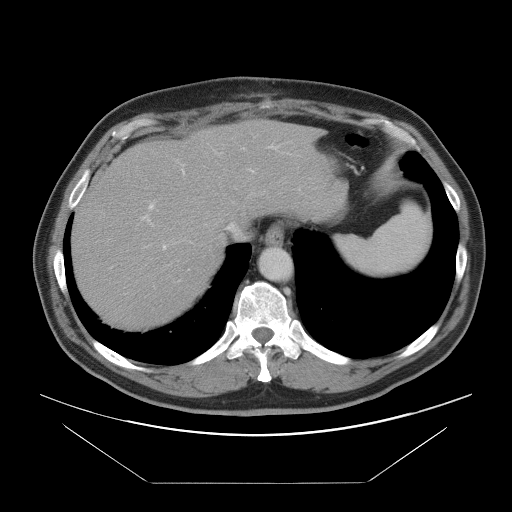
Contrast-enhanced abdominal CT, one axial slice; position 75 of 97 along the scan axis; 120 kVp; intravenous contrast given; soft-tissue window (W 400 / L 40 HU); 5 mm slice thickness; 512 × 512 image matrix, field of view 442 × 442 mm. Male patient, age 62 years. From the clinical record (not read from this slice): diagnosis: colorectal cancer liver metastases, imaged before liver resection.
Structures marked on this image (expert manual segmentation):
- hepatic veins: box from (x=226, y=152) to (x=300, y=236) px
- liver: (x=74, y=122)–(x=326, y=324)
- planned liver remnant (the part of the liver to remain after resection): (x=74, y=172)–(x=227, y=324)
- portal vein (with intrahepatic branches): (x=142, y=145)–(x=278, y=271)